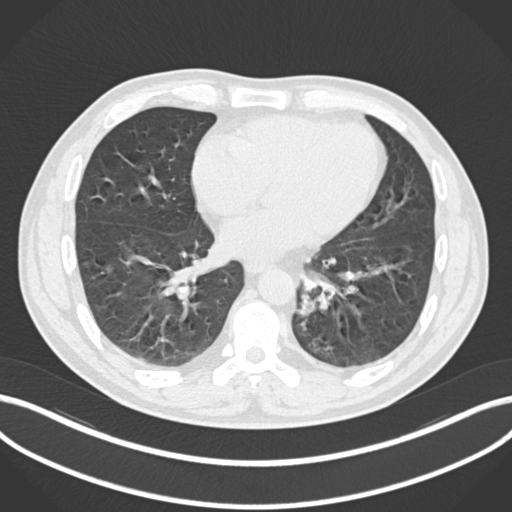
Chest CT, one axial slice; slice 74 of 223 in the series (ordered by position); reconstruction kernel B30f; 120 kVp; lung window (W 1500 / L -600 HU); 512 × 512 image matrix, field of view 400 × 400 mm. Patient: male, 50 years. From the clinical record (not read from this slice): clinical TNM (as recorded): T2a N3 M0.
Structures marked on this image (bounding box drawn by a radiologist):
- lung tumour (recorded histology: squamous cell carcinoma): box from (x=291, y=289) to (x=323, y=320) px